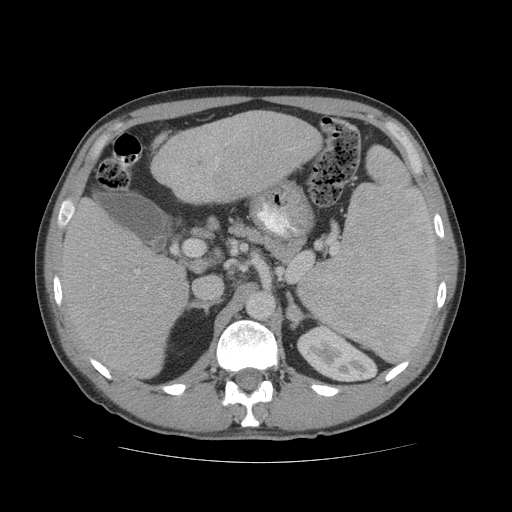
Contrast-enhanced abdominal CT (liver protocol), one axial slice. Position 34 of 81 along the scan axis. Reconstruction kernel STANDARD. 140 kVp. Soft-tissue window (W 400 / L 40 HU). 512 × 512 image matrix, field of view 400 × 400 mm. Case-level facts recorded for this patient, not image findings: diagnosis: hepatocellular carcinoma (patient treated with transarterial chemoembolisation; whether this scan precedes or follows treatment is not stated here); TNM stage (as recorded): Stage-IVB; Child-Pugh class: B; tumour nodularity: multinodular.
Structures marked on this image (semi-automatically segmented with operator editing):
- liver parenchyma outside the tumour (the mass and vessels are separate outlines, so this box may not span the whole liver): bounding box [x1, y1, x2, y2] px = [56, 110, 322, 378]
- liver vessels: [136, 135, 291, 273]